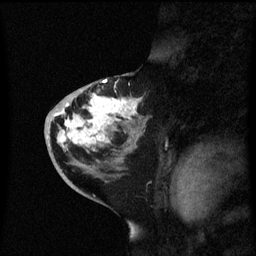
Breast MRI (dynamic contrast-enhanced), one sagittal slice; slice 31 of 60 in the series (ordered by position); dynamic contrast-enhanced series, image 2 of 3 at this slice position (ordered by acquisition); 1.5 T; TE 4.2 ms, TR 8.4 ms; 2.3 mm slice thickness; 256 × 256 image matrix. Patient: female, 46 years. Case-level facts recorded for this patient, not image findings: setting: breast cancer imaged before/during neoadjuvant chemotherapy; receptor status: HER2-positive.
Outlined on this slice (semi-automatically segmented with operator editing):
- analysis volume of interest (the breast-tissue region the enhancement analysis was run in; not a lesion): bounding box <44,86,151,171> (left, top, right, bottom; pixels)
- tumour enhancement mask (voxels above the 70 % enhancement threshold inside the analysis volume of interest): <56,94,135,147>